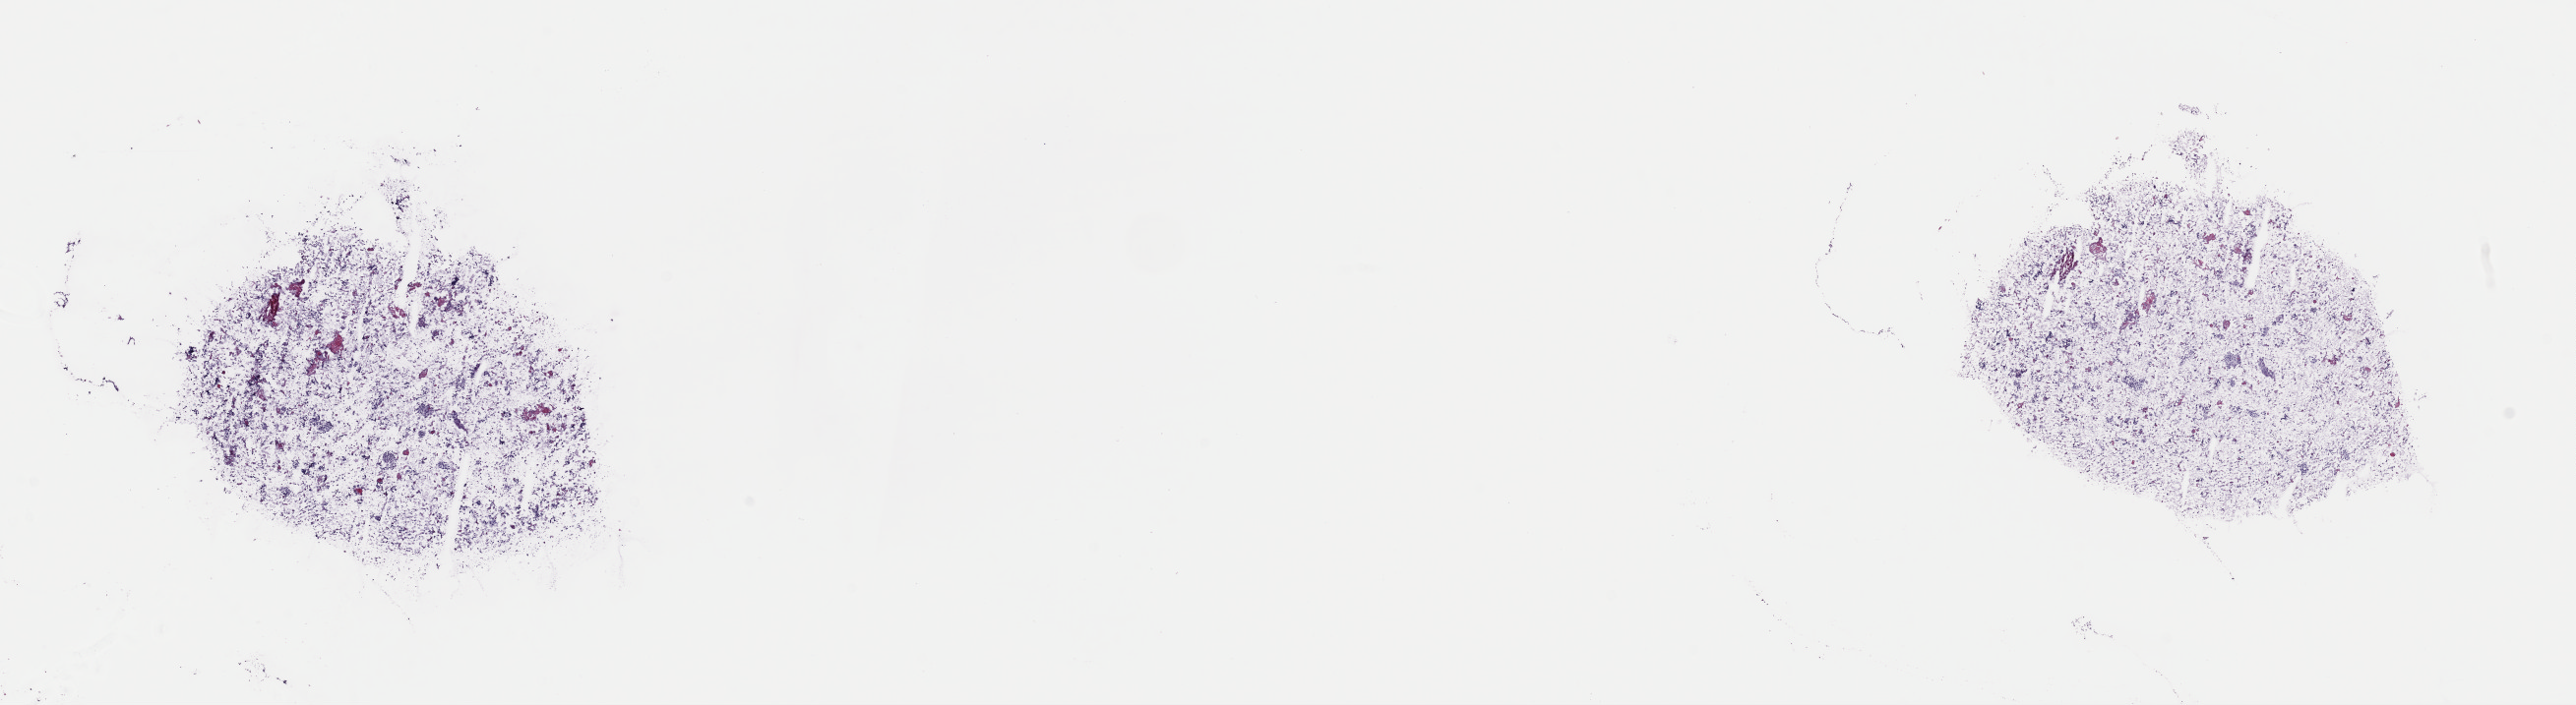
Whole-slide histology image, H&E — low-resolution overview of the scanned area, about 20.7 x 5.7 mm (acquisition: 40x scan). Frozen section from the top of the tissue portion. Sample: primary tumour, bladder. Female, age 80 years at initial diagnosis. Histologic grade: high grade. Slide review estimates, as recorded: tumour cells 85%, tumour nuclei 65%, normal cells 0%, stromal cells 0%, necrosis 15%. Infiltration values recorded for this section: lymphocyte infiltration 8%, monocyte infiltration 1%, neutrophil infiltration 1%.
Histologic diagnosis: Transitional cell carcinoma. AJCC pathologic stage: III (7th edition).